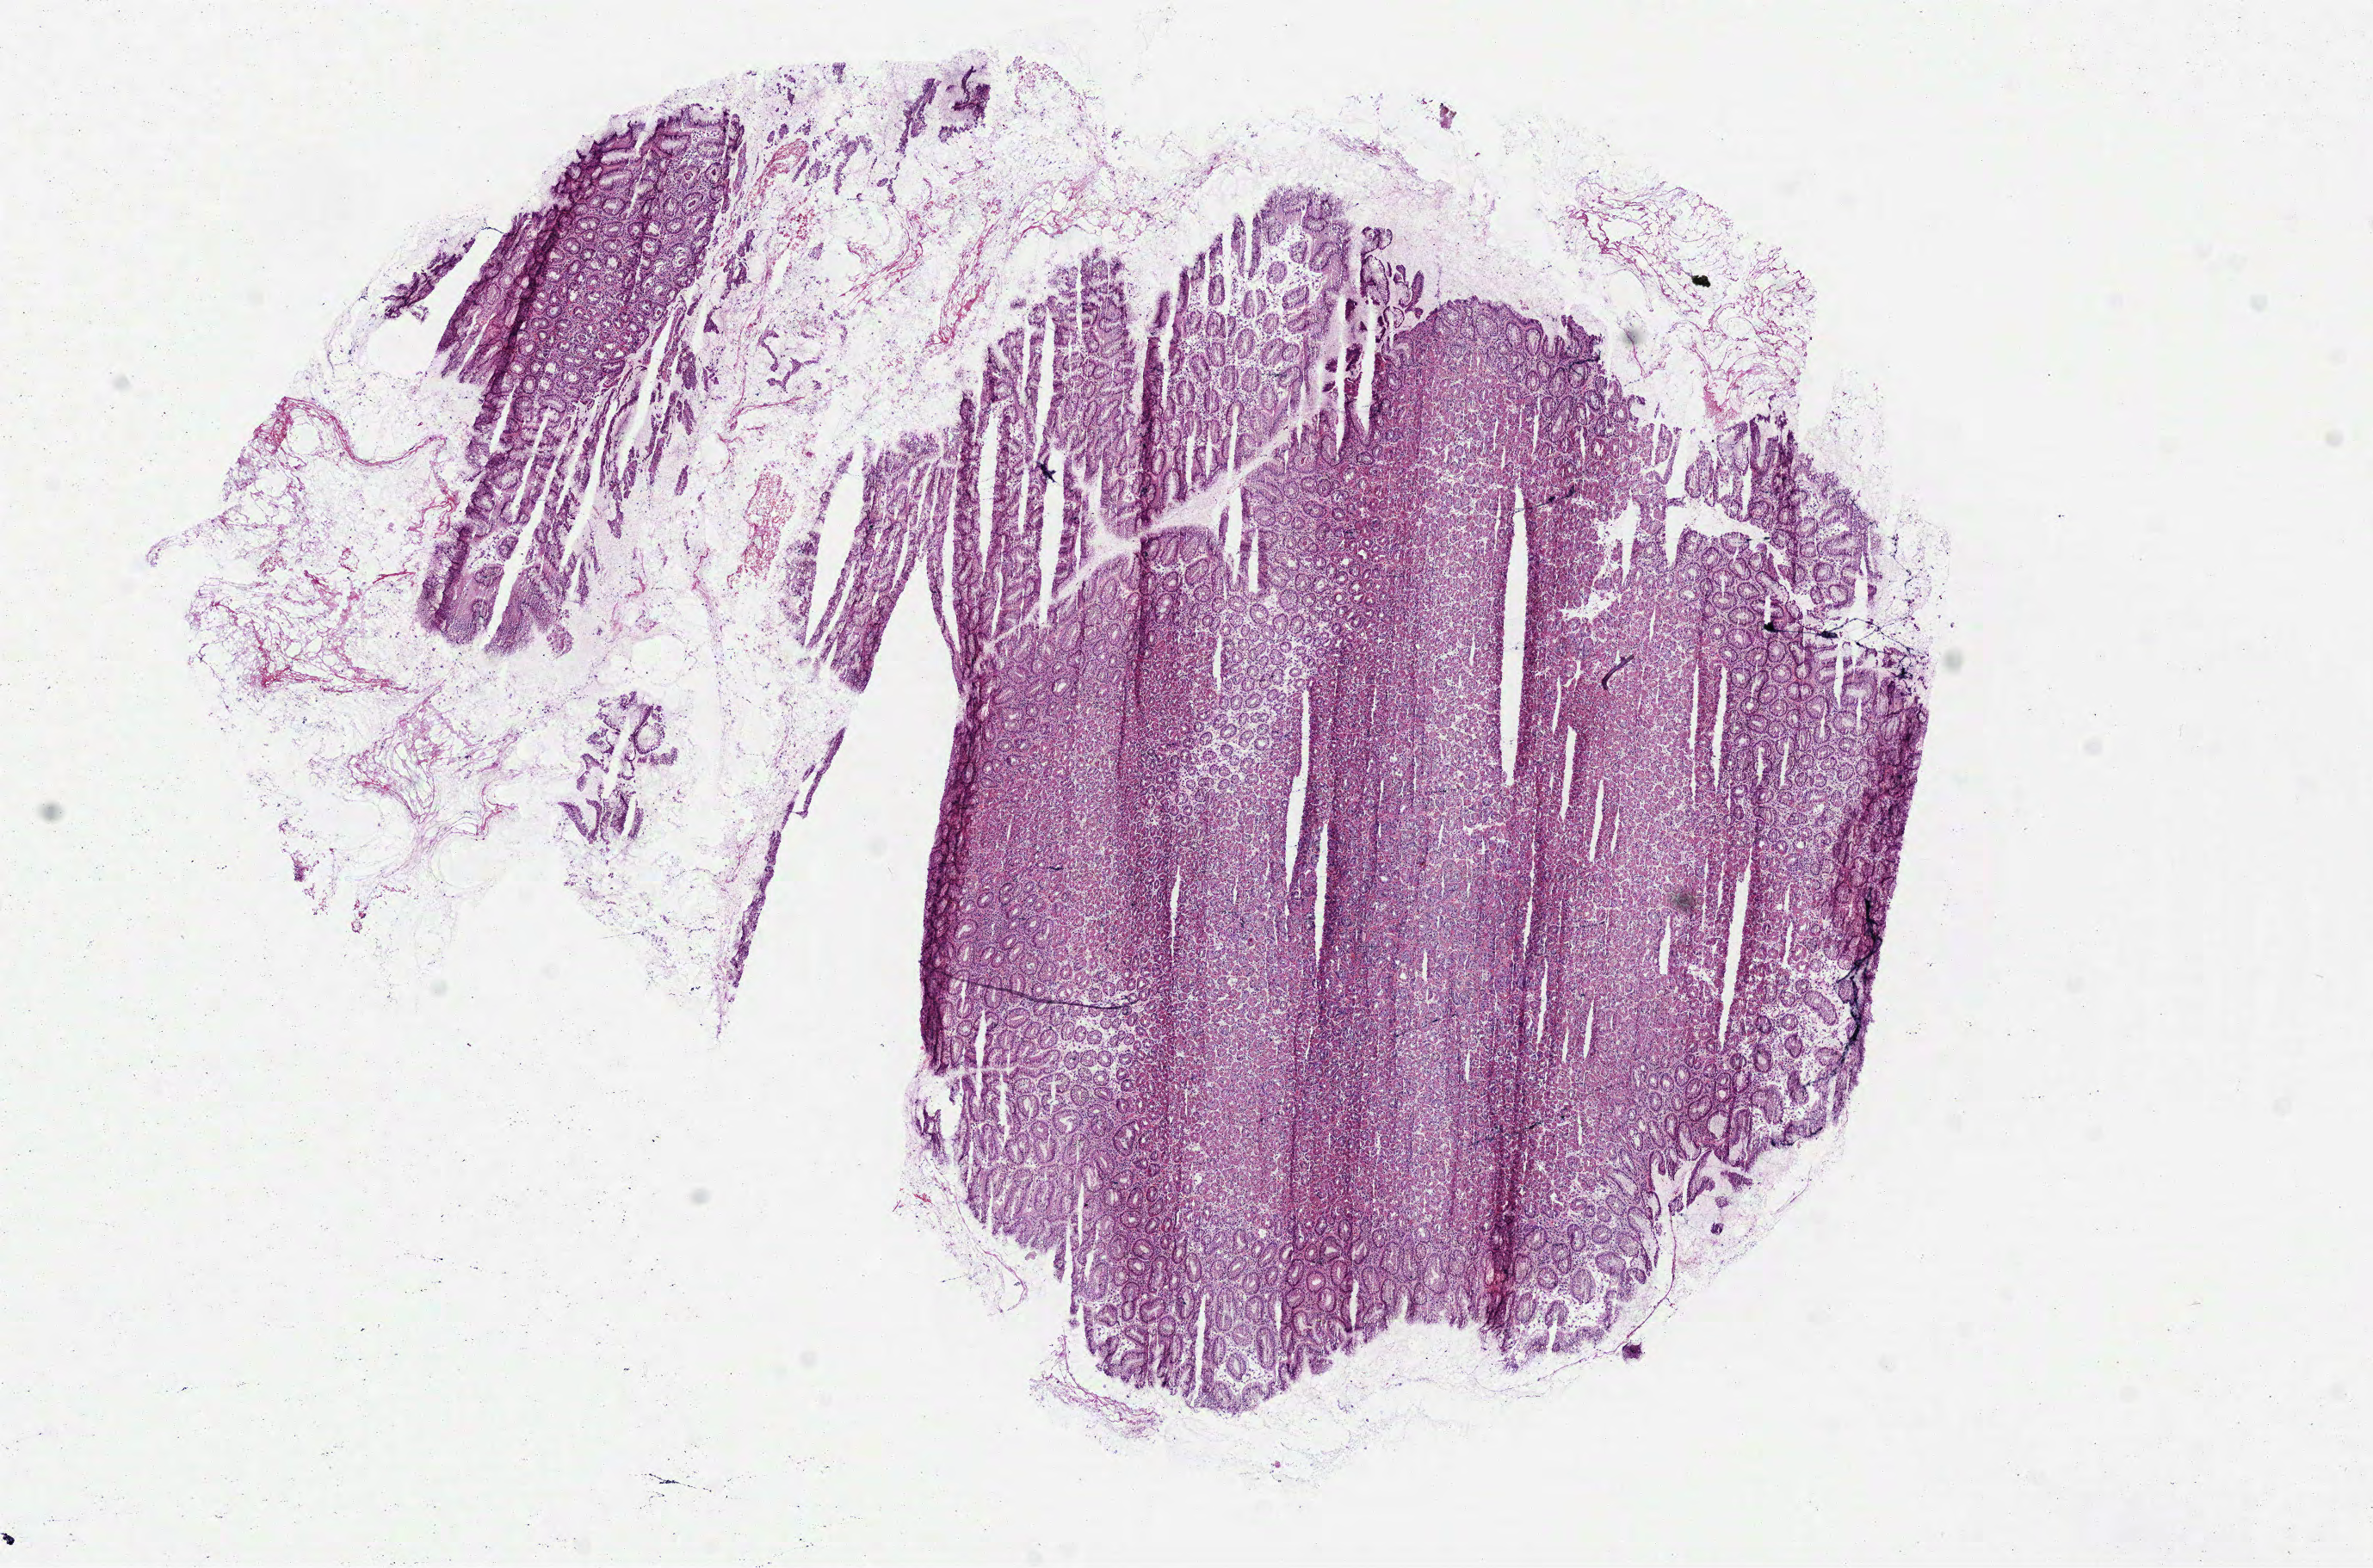
H&E-stained whole-slide image — a low-resolution overview of the entire scanned area, about 11.1 x 7.3 mm (from a 40x scan), frozen section, sample: solid tissue normal (non-tumour tissue), stomach. Female, age 71 years at initial diagnosis.
This section: solid tissue normal (non-tumour) sample from the same patient. Patient diagnosis: Adenocarcinoma, intestinal type (gastric antrum).